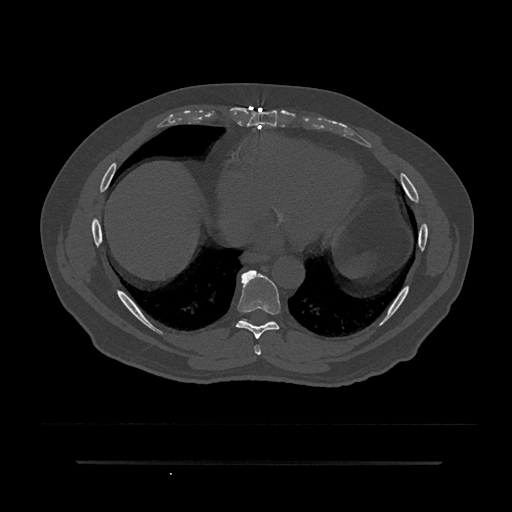
CT including the spine, one axial slice; position 420 of 797 along the scan axis; 120 kVp; bone window (W 1800 / L 400 HU); 512 × 512 image matrix, field of view 464 × 464 mm. Patient: male, 59 years. From the clinical record (not read from this slice): primary cancer: bile ducts; vertebrae with lytic lesions (as recorded): T10.
Annotated regions visible in this slice (semi-automatically segmented with operator editing):
- T7 vertebra: box from (x=254, y=345) to (x=261, y=355) px
- T8 vertebra: (x=236, y=270)–(x=281, y=339)